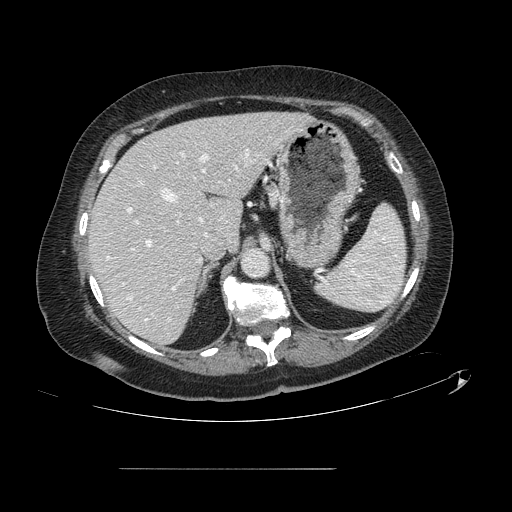
Contrast-enhanced abdominal CT, one axial slice; position 90 of 148 along the scan axis; 120 kVp; intravenous contrast given; soft-tissue window (W 400 / L 40 HU); 2.5 mm slice thickness; 512 × 512 image matrix. Female patient, age 75 years. From the clinical record (not read from this slice): diagnosis: colorectal cancer liver metastases, imaged before liver resection; multiple liver metastases: no; largest metastasis: 2.4 cm.
Outlined on this slice (manually delineated by an expert):
- hepatic veins: bounding box [x1, y1, x2, y2] px = [129, 153, 238, 321]
- liver: [90, 113, 308, 344]
- planned liver remnant (the part of the liver to remain after resection): [90, 113, 308, 344]
- portal vein (with intrahepatic branches): [128, 148, 259, 290]